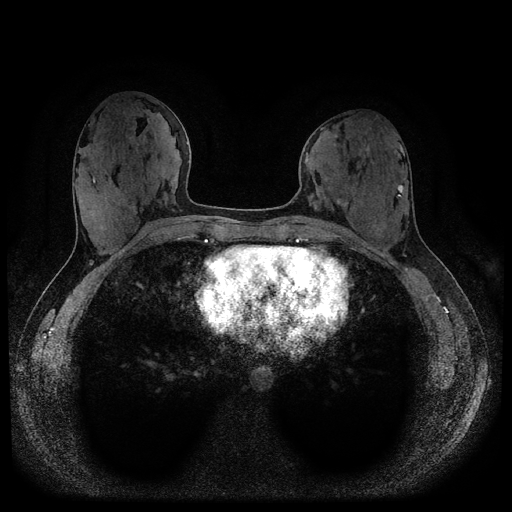
Breast MRI (dynamic contrast-enhanced, multi-phase), one axial slice. Position 40 of 116 along the scan axis. Dynamic contrast-enhanced series, time point 2 of 5 at this slice position (early post-contrast). 1.5 T. TE 2.6 ms, TR 5.3 ms. 2 mm slice thickness. 512 × 512 image matrix. Female patient, age 33 years.
Outlined on this slice (semi-automatically segmented with operator editing):
- breast lesion (labelled benign in the annotation): bounding box <335,198,349,209> (left, top, right, bottom; pixels)